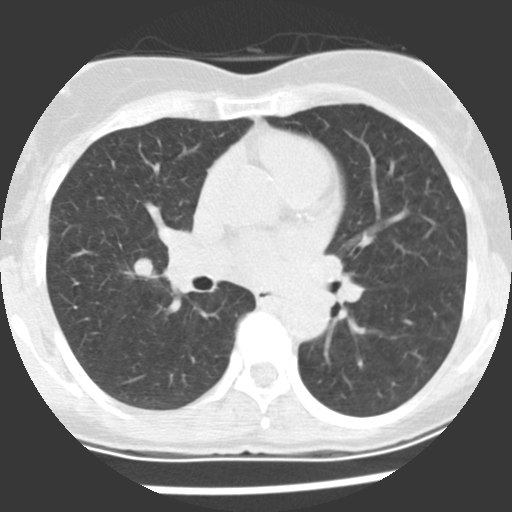
Low-dose screening chest CT, one axial slice; slice 119 of 225 in the series (ordered by position); 120 kVp; lung window (W 1500 / L -600 HU); 2.5 mm slice thickness; 512 × 512 image matrix.
Annotated regions visible in this slice (outlined manually by an expert reader):
- lesion 1 (tumor, upper lobe of right lung): bounding box (x1, y1, x2, y2) in pixels: (134, 258, 154, 280)